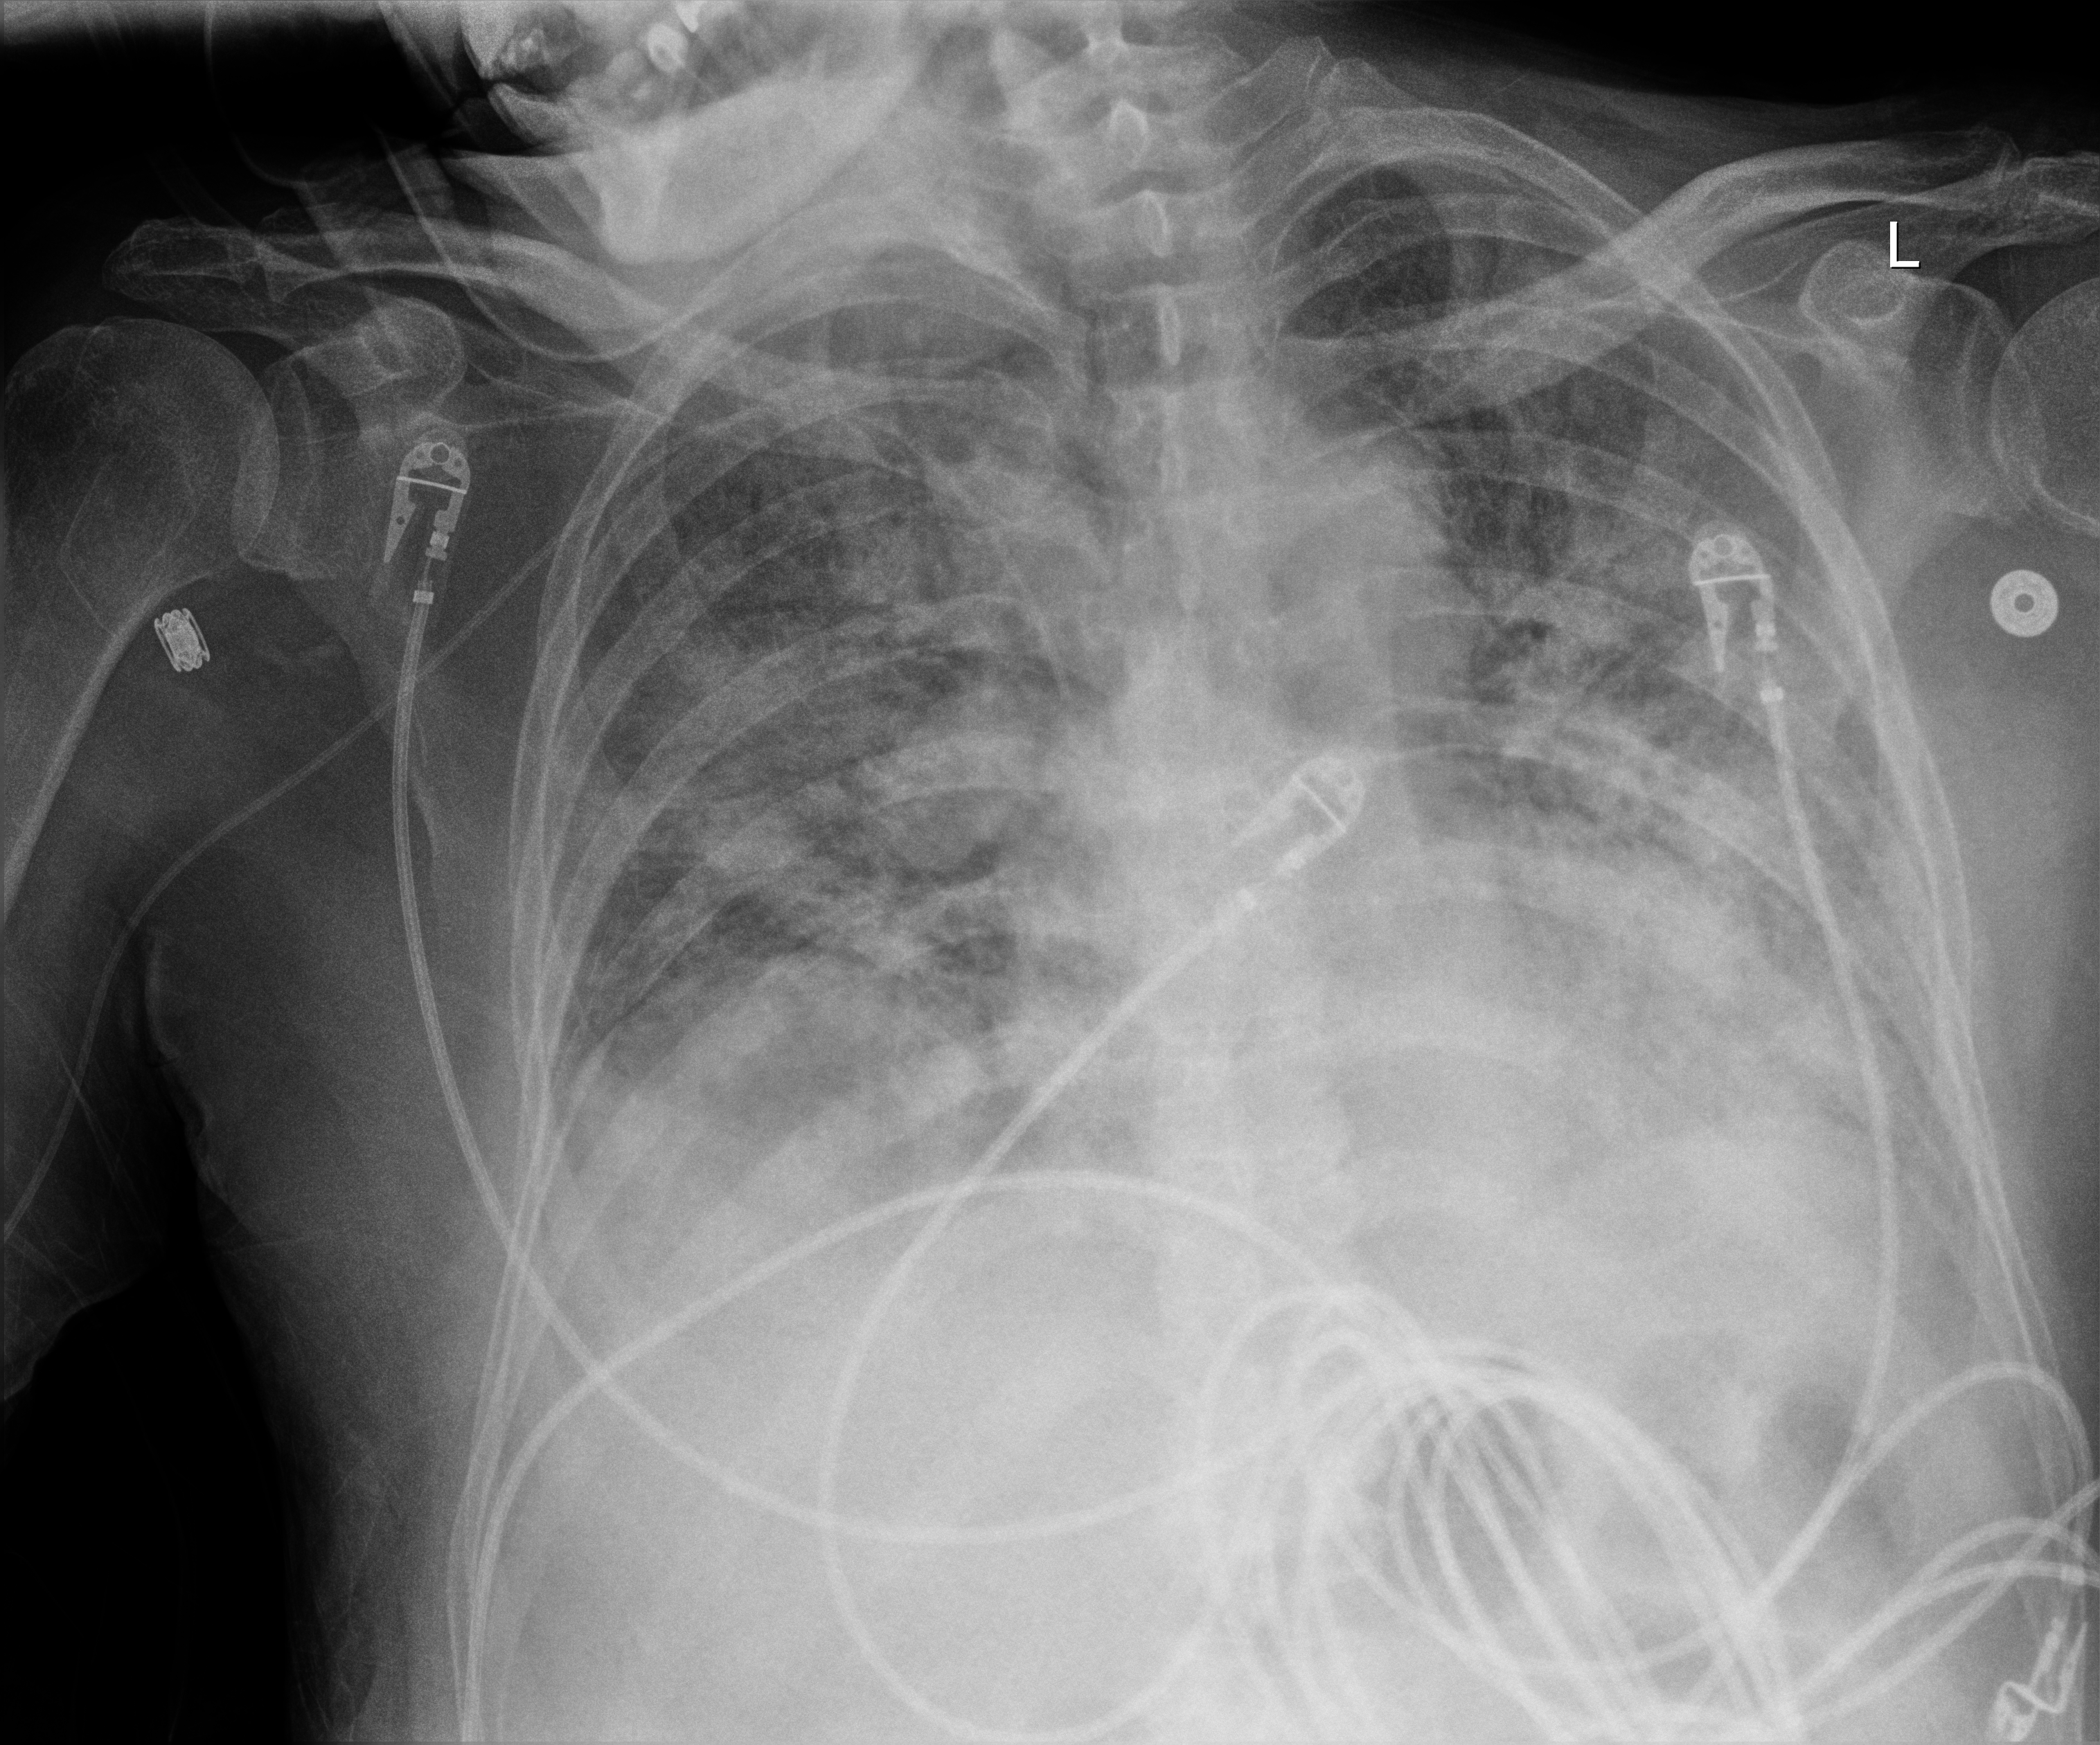
Chest X-ray, anteroposterior (AP) projection. Patient hospitalised with COVID-19; male, aged 60–74 years.
From the hospital-stay record, not from the radiograph (when in the stay this image was taken is not recorded):
- mechanically ventilated during this hospital stay: yes
- diabetes (admission record): no
- COPD (admission record): no